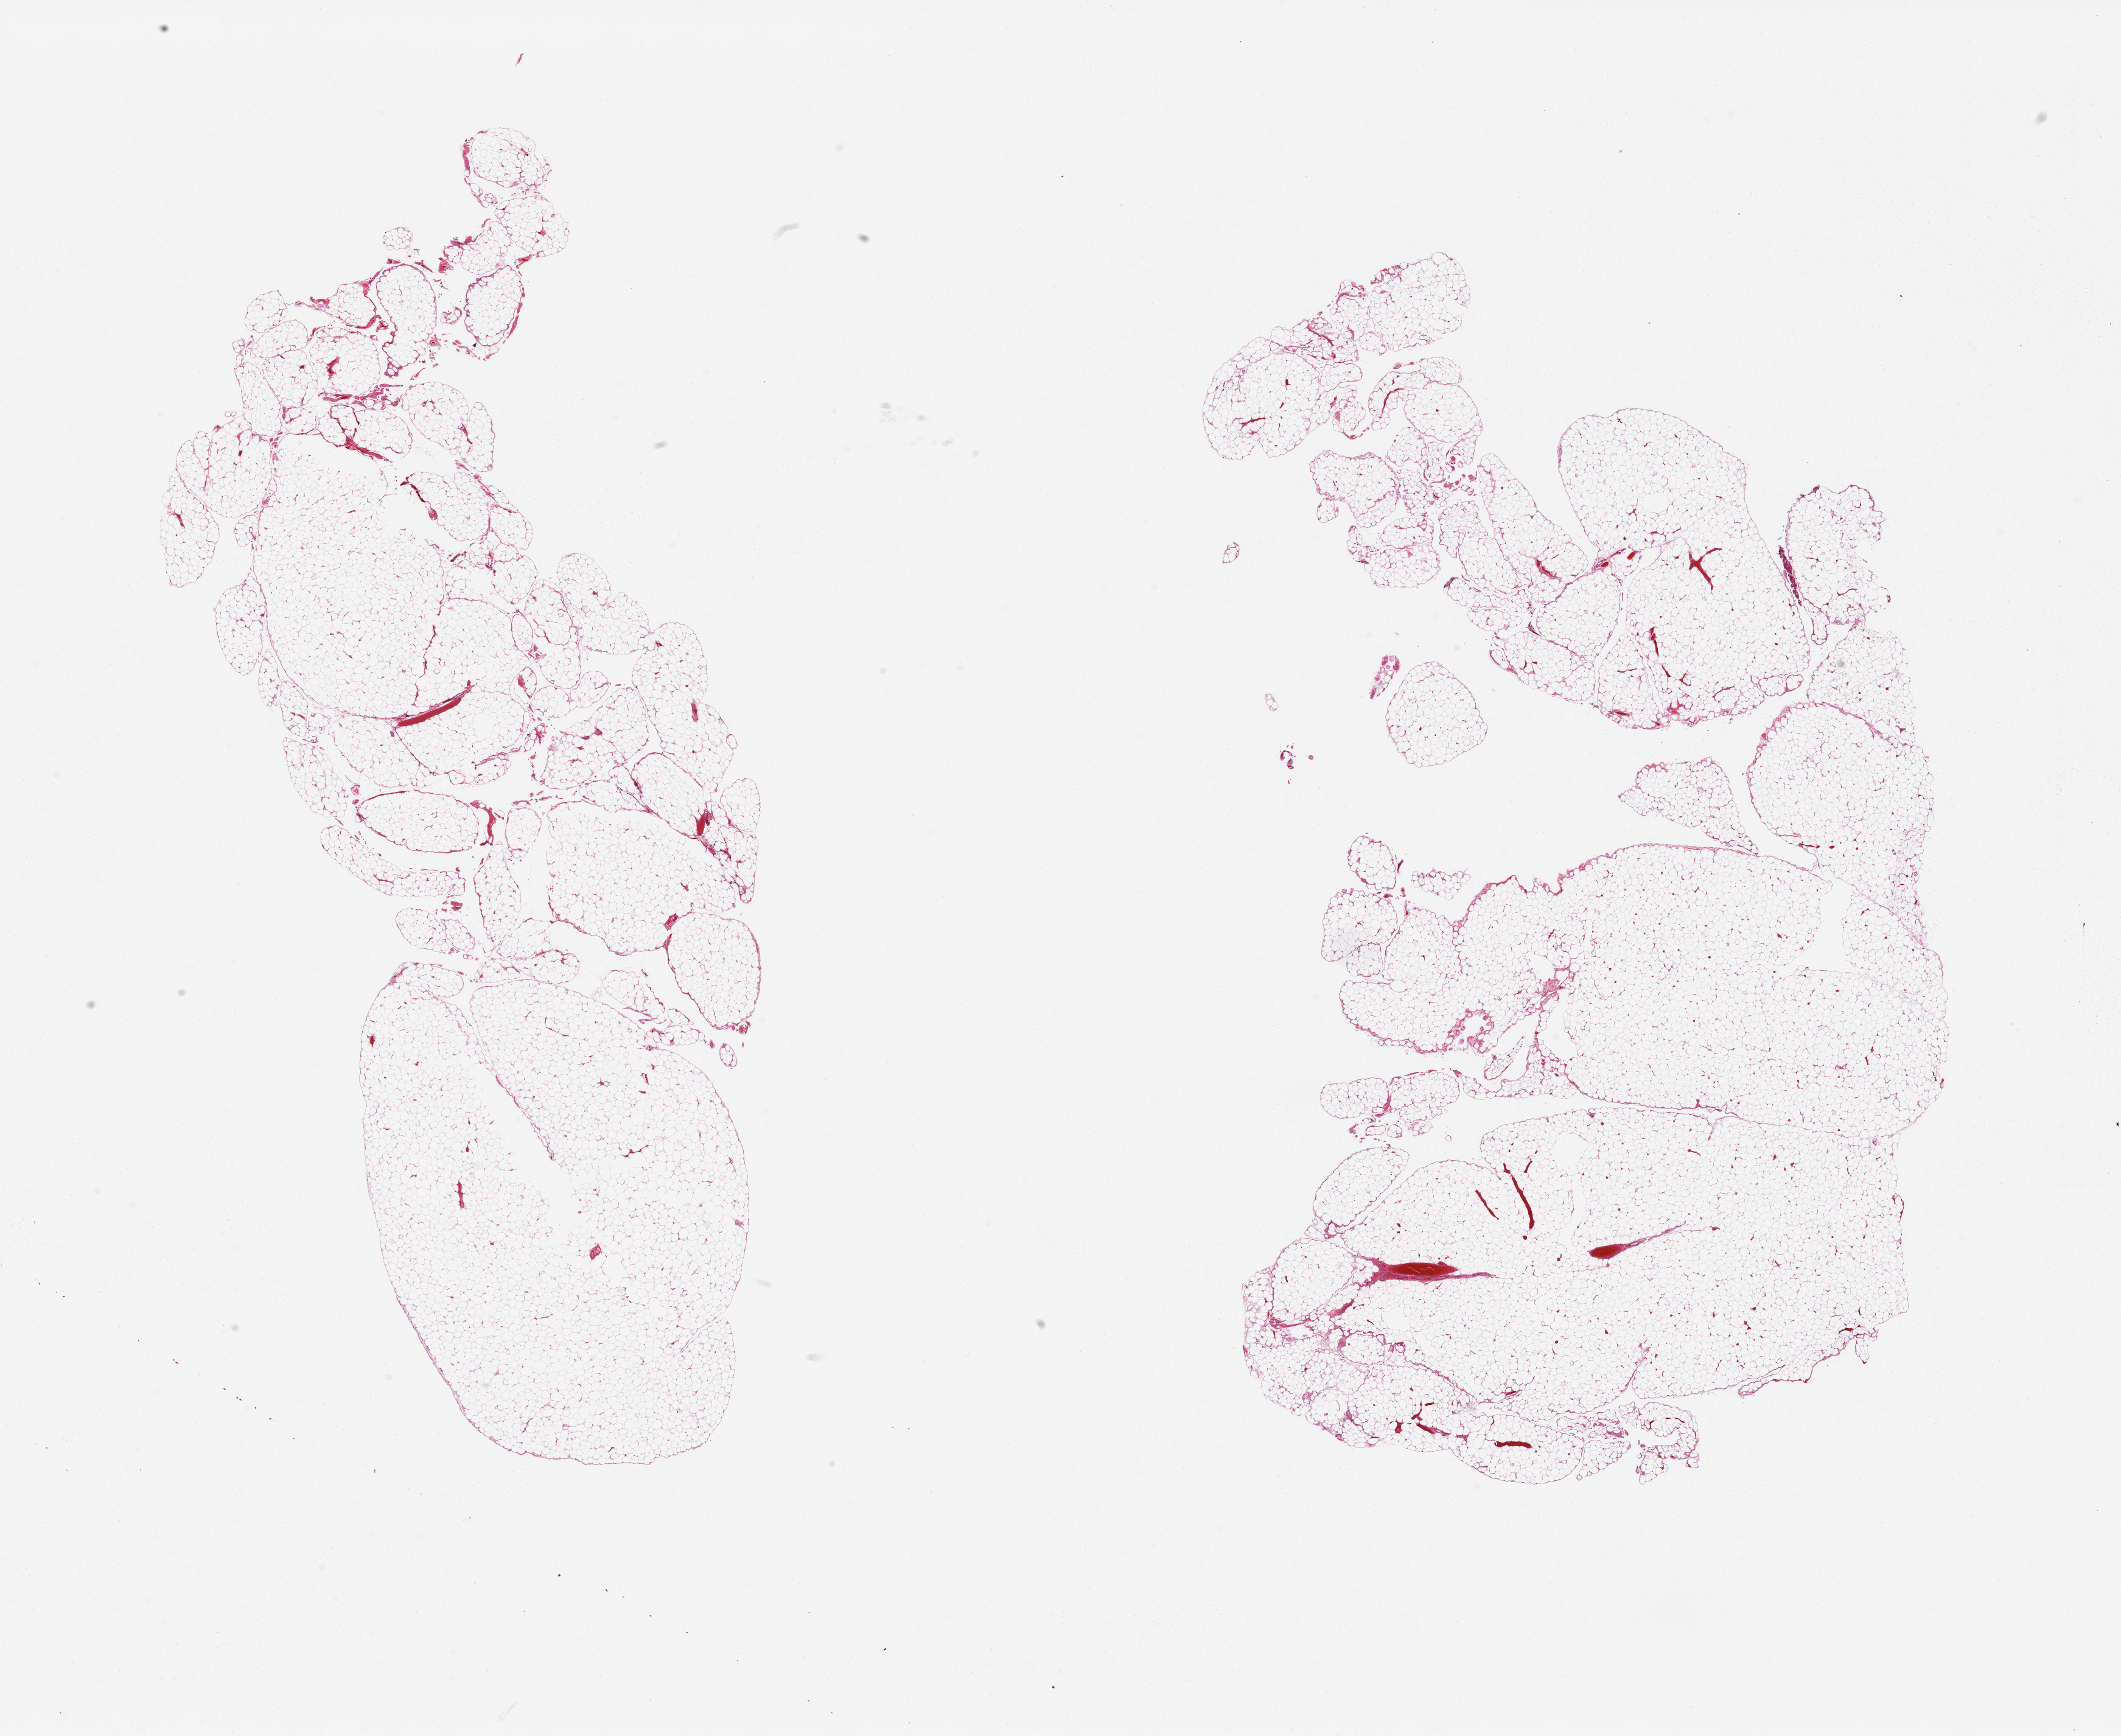
Whole-slide image, H&E stain — whole scanned area (about 27.6 x 22.6 mm) shown as a low-resolution overview. PAXgene-fixed, paraffin-embedded tissue. Section of omentum (target tissue). Donor tissue sample.
- review note (as recorded): 2 pieces; minimal stromal content